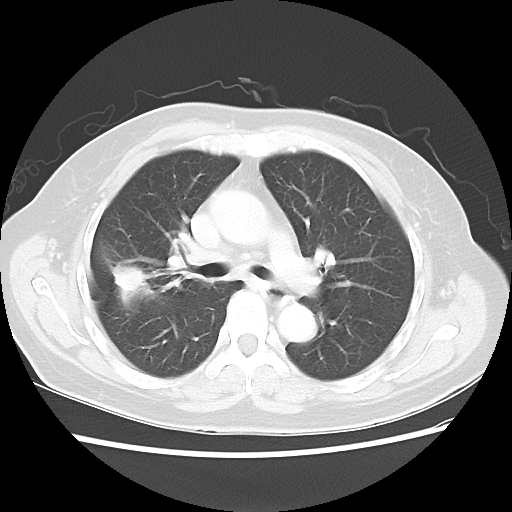
Chest CT, one axial slice; position 21 of 40 along the scan axis; reconstruction kernel LUNG; lung window (W 1500 / L -600 HU); 512 × 512 image matrix, field of view 342 × 342 mm. Patient: female, 67 years. Case-level facts recorded for this patient, not image findings: clinical TNM (as recorded): T1c N1 M0.
Annotated regions visible in this slice (rectangle marked by the reading radiologist):
- lung tumour (recorded histology: adenocarcinoma): bounding box <104,252,159,318> (left, top, right, bottom; pixels)